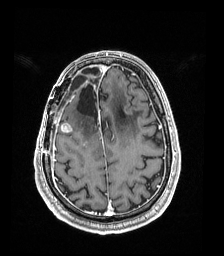
Brain MRI from a brain-tumour surgery series, one axial slice; slice 51 of 192 in the series (ordered by position); T1-weighted post-contrast; 224 × 256 image matrix. From the clinical record (not read from this slice): histopathology: Astrocytoma; WHO grade: 4; IDH mutation: yes.
Structures marked on this image (expert manual segmentation):
- previous resection cavity: box from (x=77, y=85) to (x=98, y=121) px